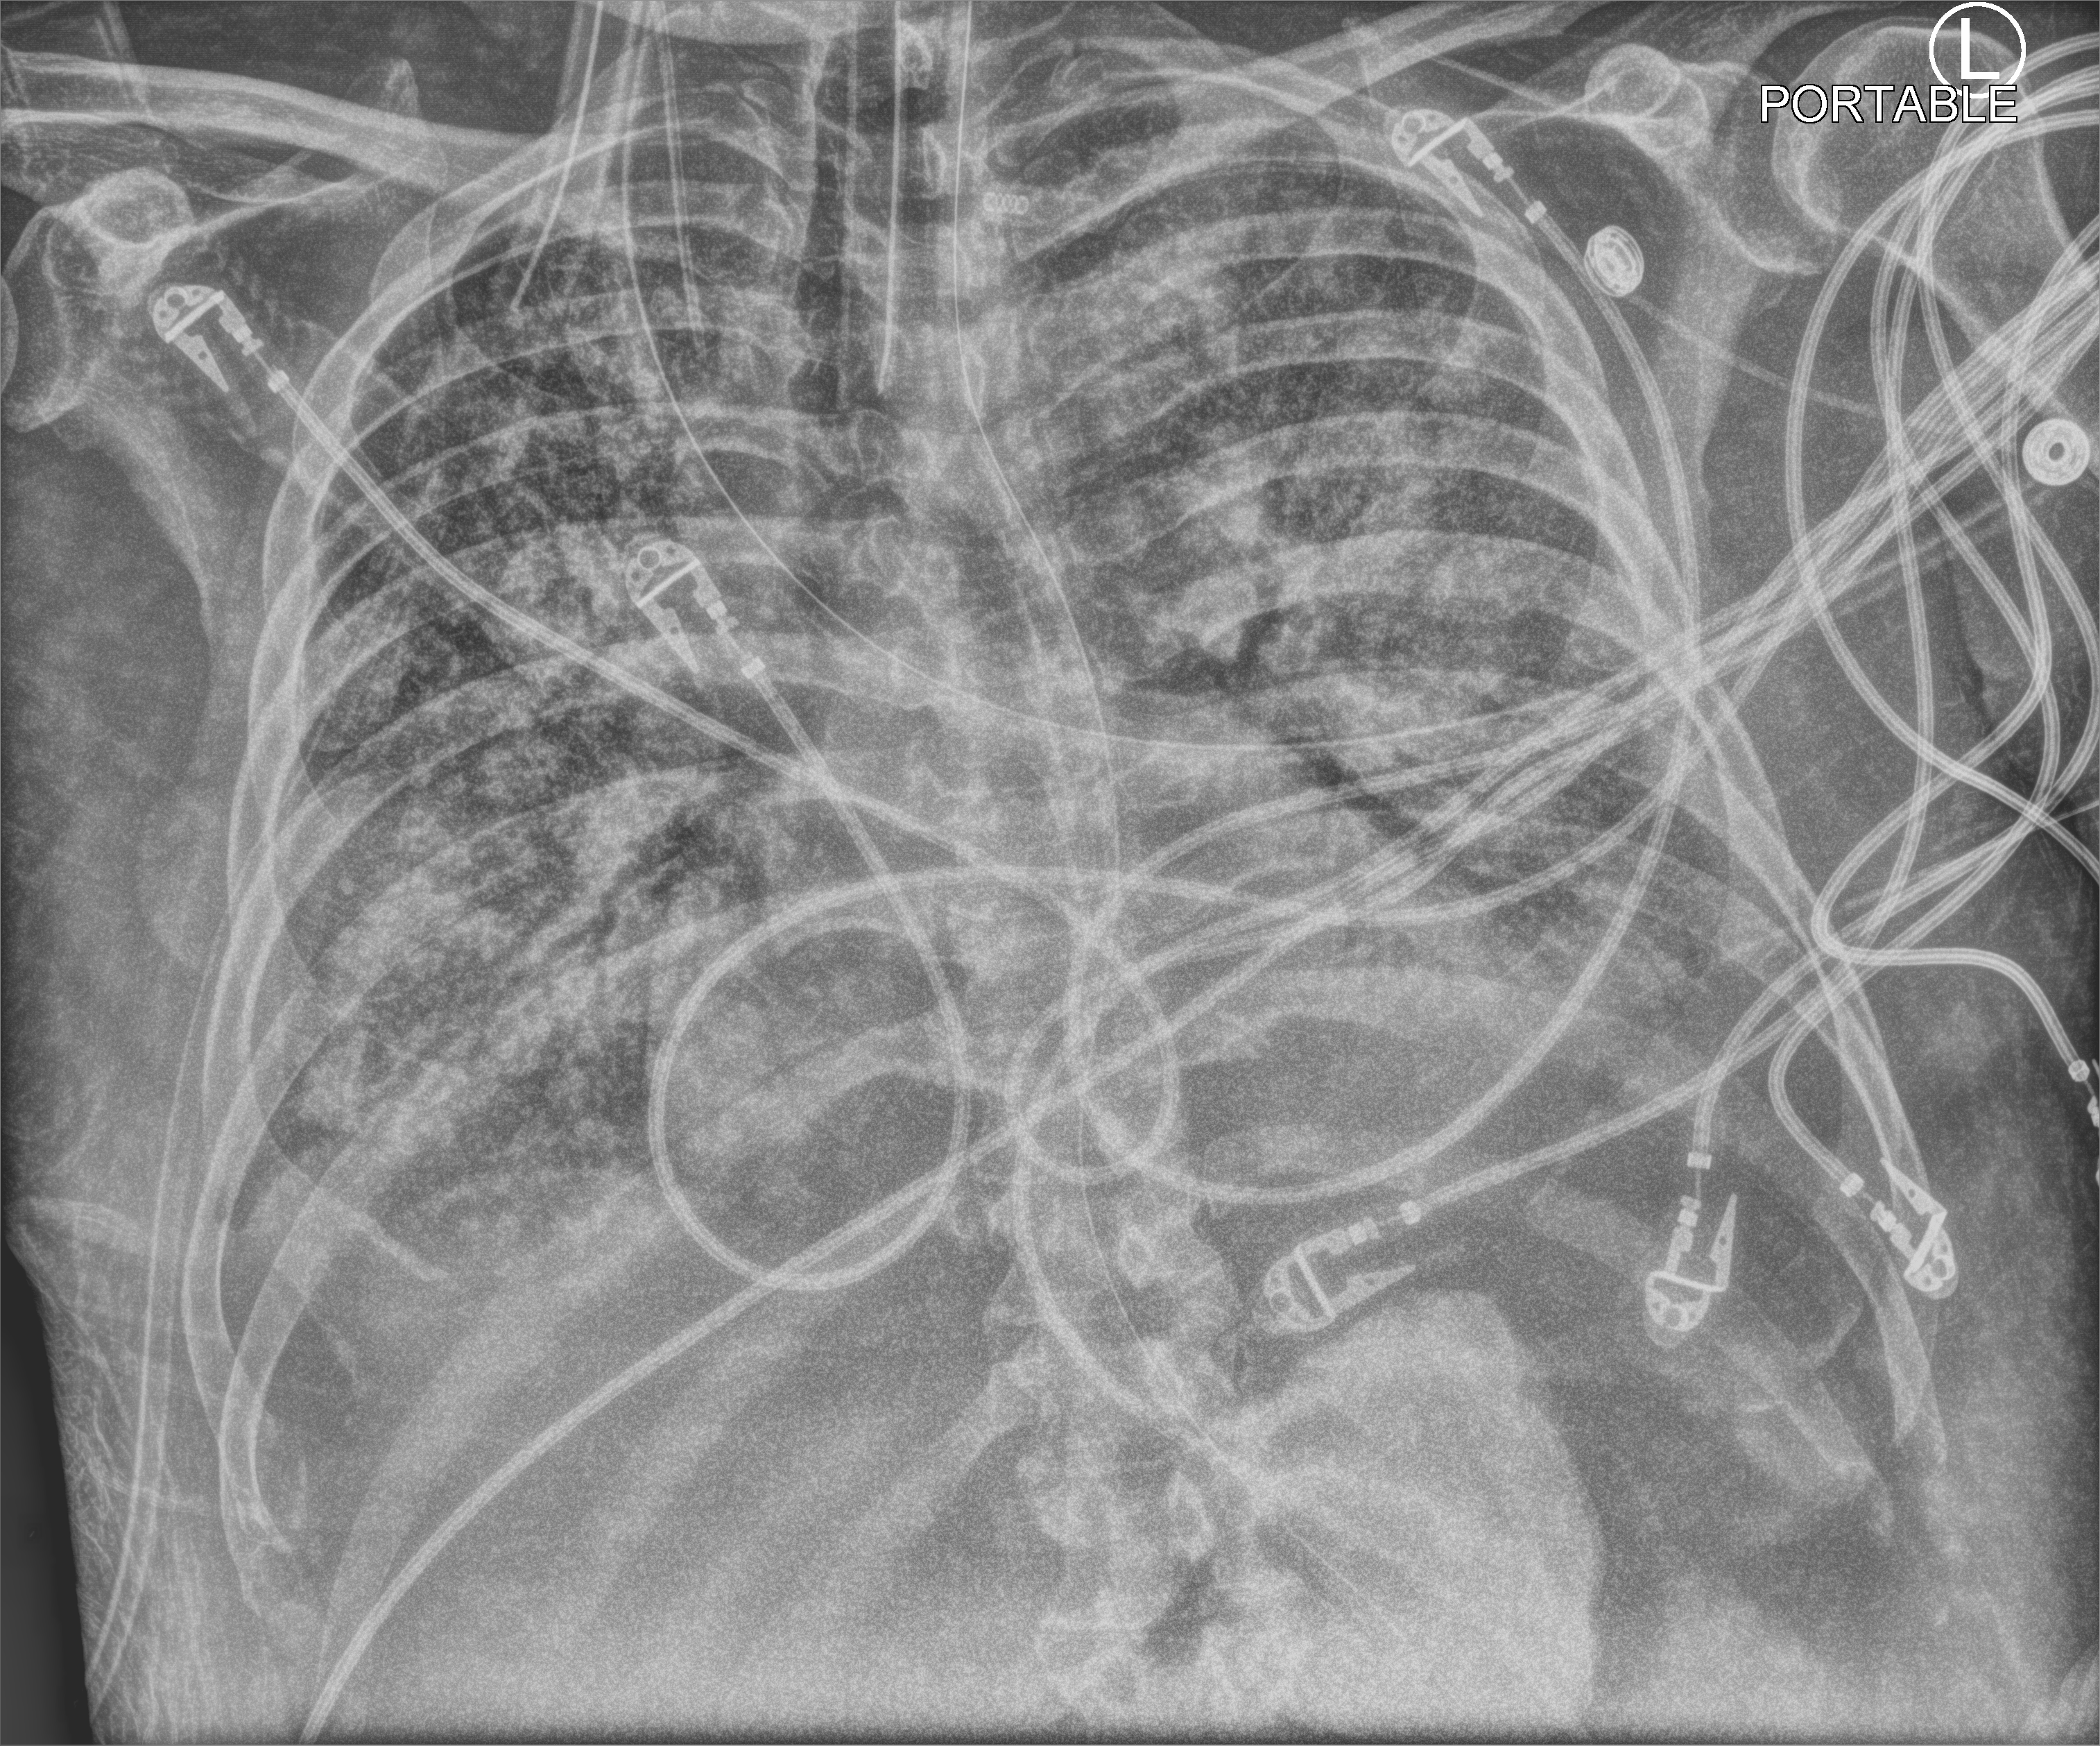
Bedside chest radiograph (computed radiography), anteroposterior (AP) projection. Patient hospitalised with COVID-19; male, aged 60–74 years.
From the hospital-stay record, not from the radiograph (when in the stay this image was taken is not recorded): admitted to intensive care during this hospital stay: yes; hypertension (admission record): yes.